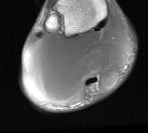
MRI of an extremity soft-tissue mass, one axial slice. Slice 15 of 76 in the series (ordered by position). MR volume resampled by the dataset authors to the PET/CT grid (not the native acquisition matrix). 3.27 mm slice thickness. 148 × 133 image matrix. Male patient. Case-level facts recorded for this patient, not image findings: histological type: liposarcoma - round cell; grade: high; site of the primary tumour: right calf.
Outlined on this slice (expert contour drawn on MRI and transferred to this co-registered scan by the dataset authors):
- gross tumour volume (mass): bounding box (x1, y1, x2, y2) in pixels: (24, 21, 130, 106)